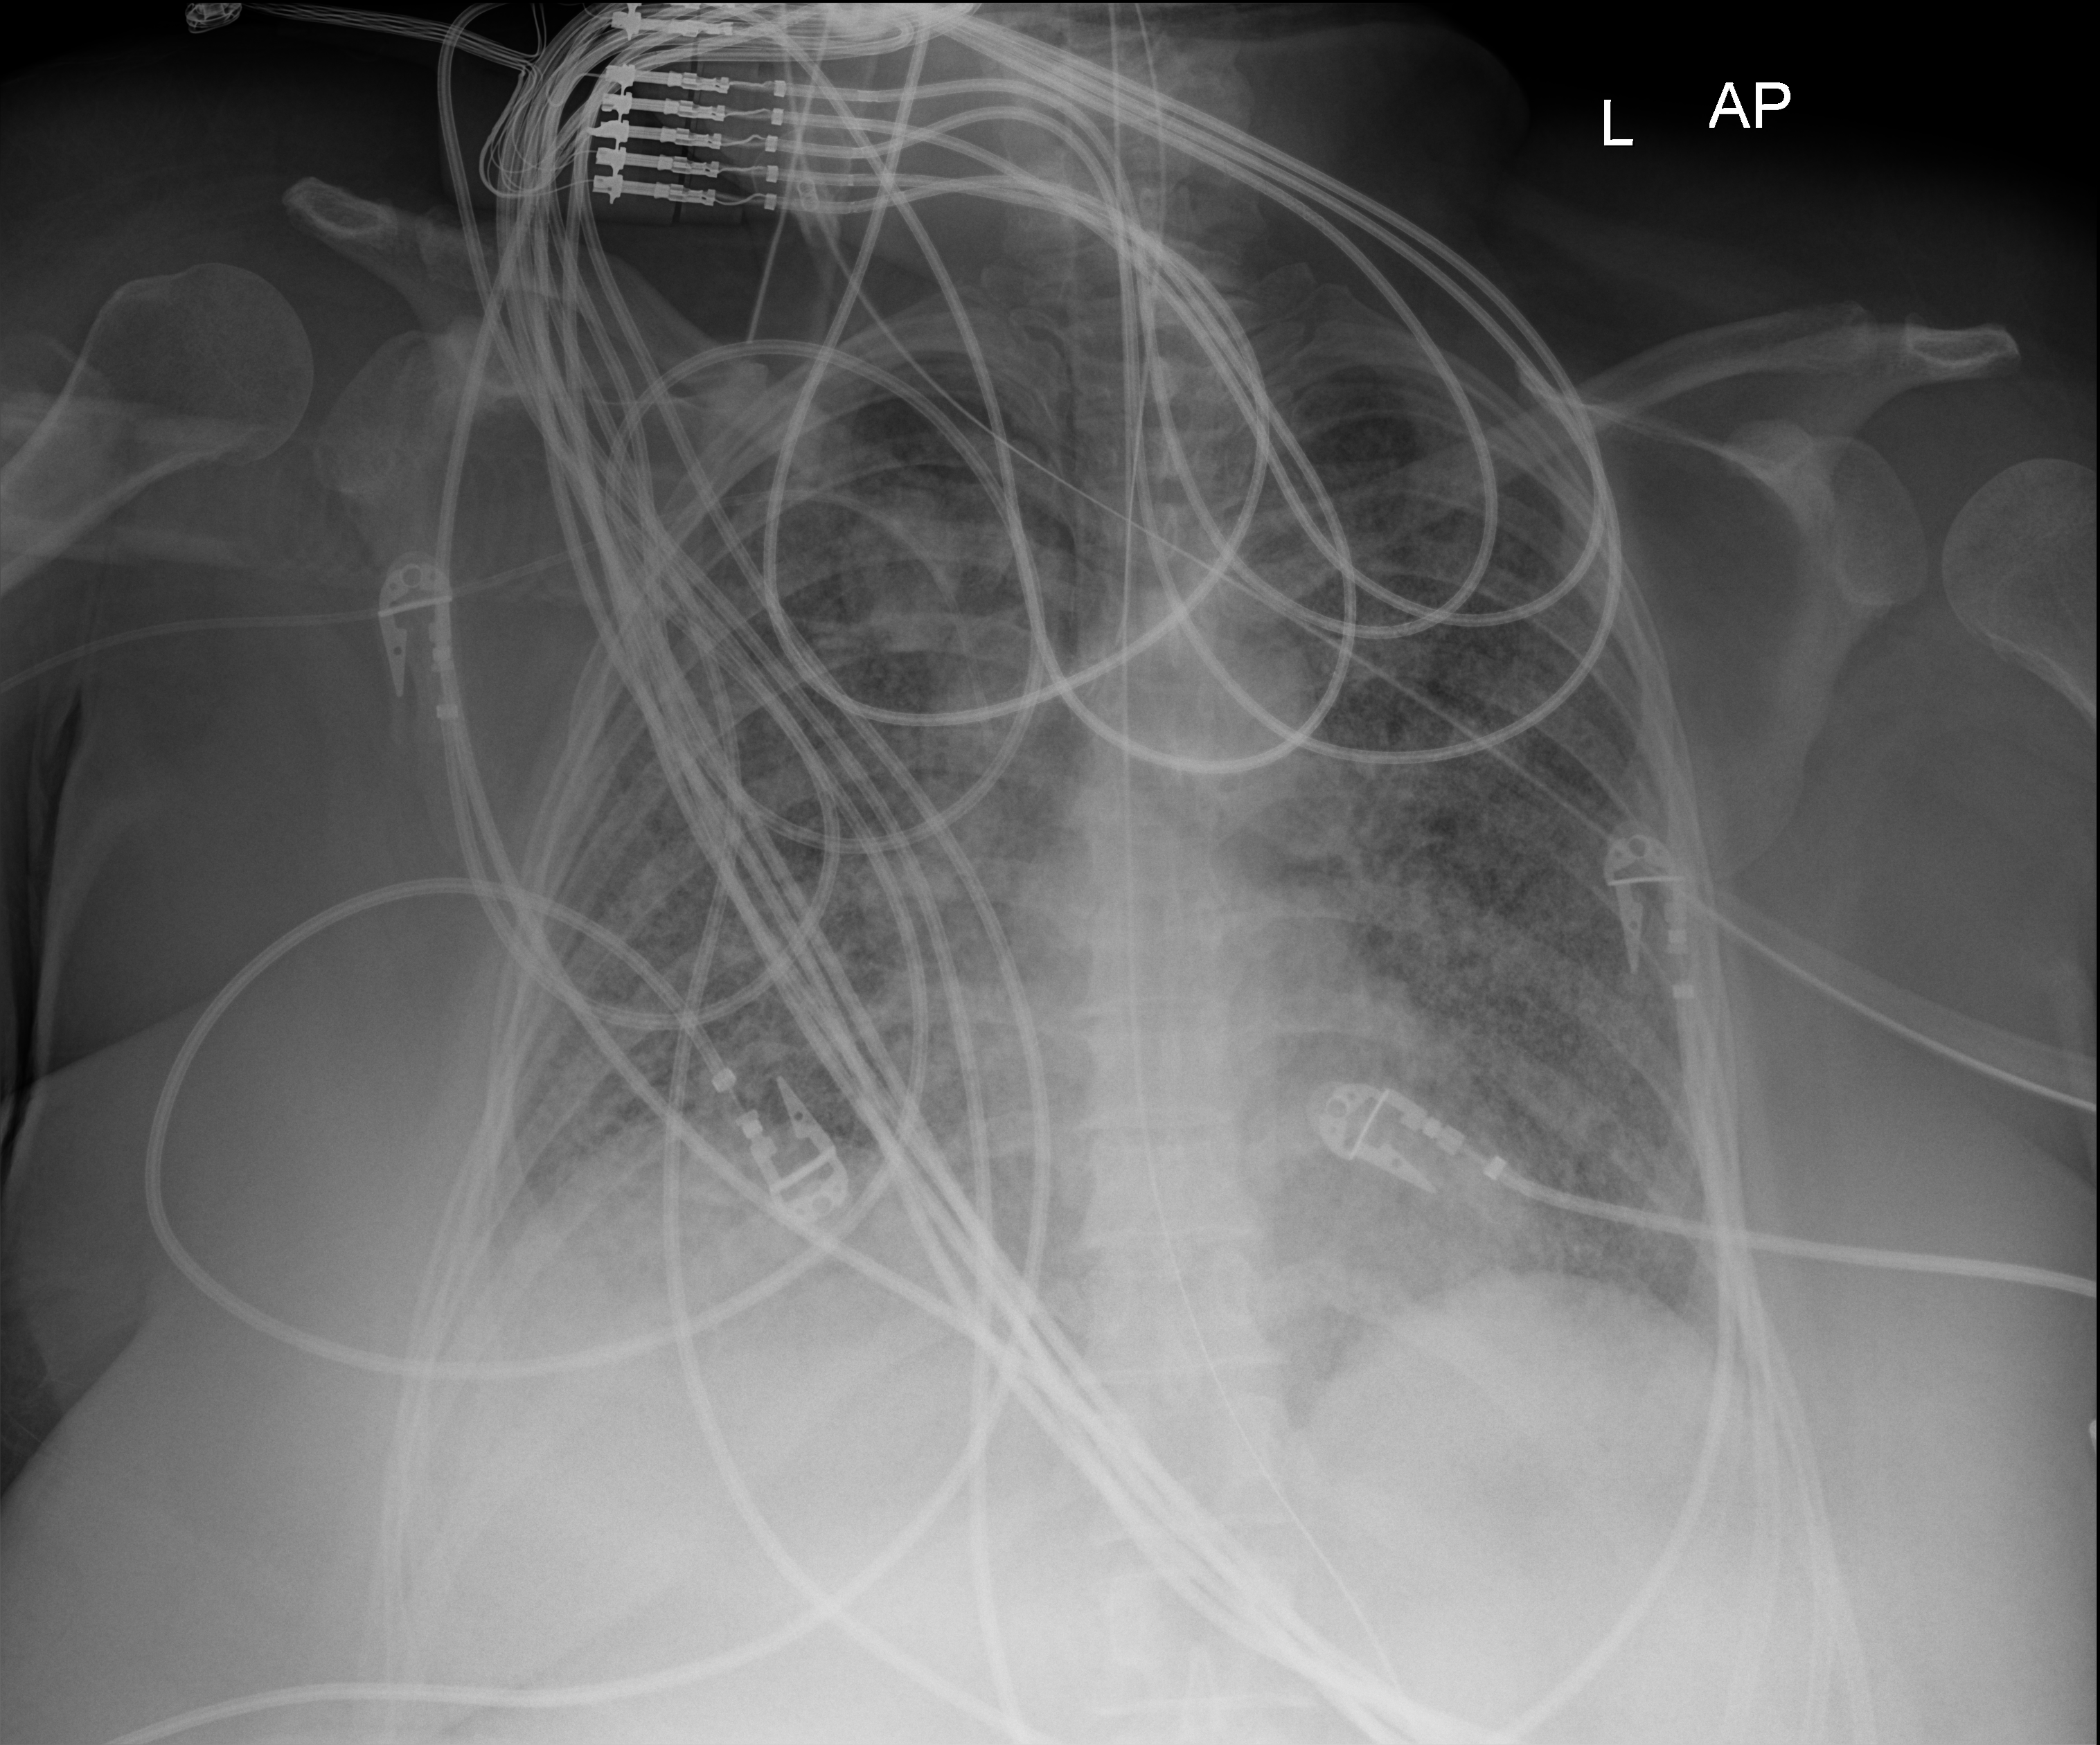
Chest X-ray (portable), anteroposterior (AP) projection. Female patient hospitalised with COVID-19, age 18–59 years.
Hospital-stay facts (about this admission, not read from this image; timing relative to this image not recorded):
- length of hospital stay: 95 days